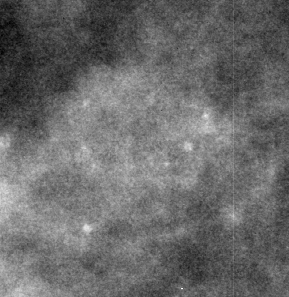
Cropped region of a digitized screen-film mammogram centred on a radiologist-marked abnormality; right breast; CC view; BI-RADS breast density category 2 (scale 1–4).
Marked abnormality: calcifications, morphology round and regular, distribution clustered; BI-RADS assessment category 3; subtlety rating 3 on a 1 (subtle) to 5 (obvious) scale; pathology result (as recorded, not read from the image): benign.